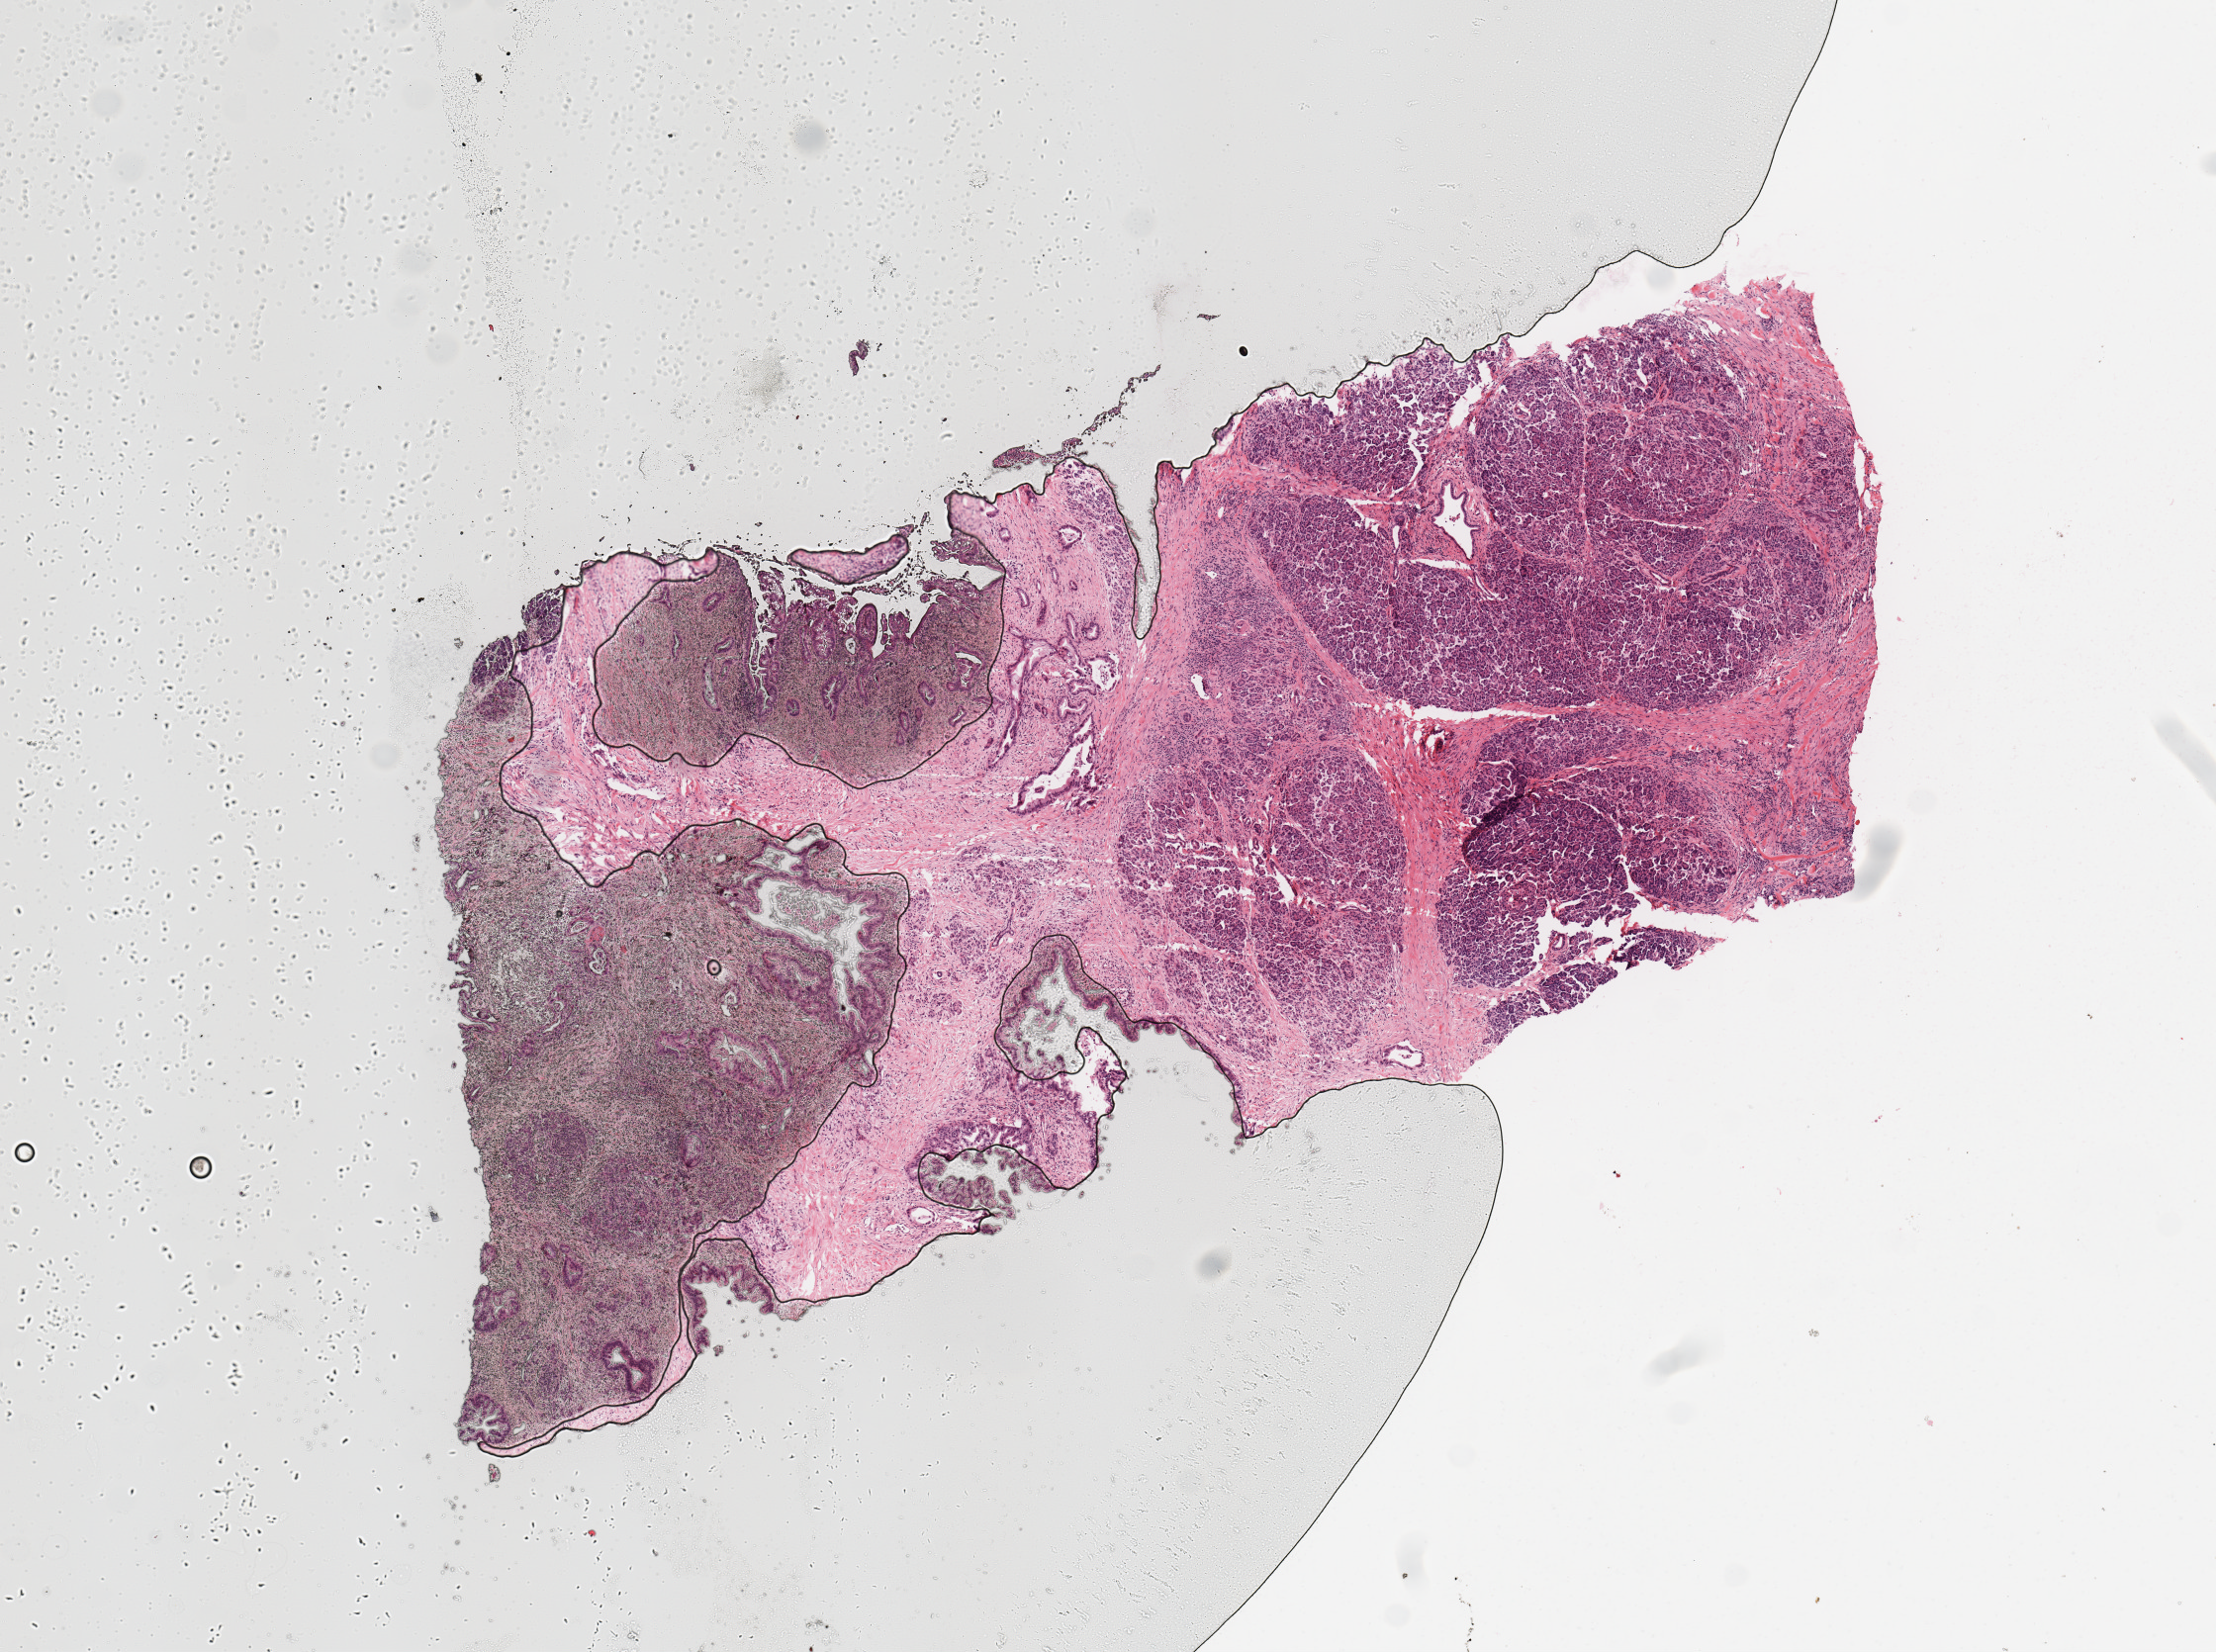
Digitized H&E-stained tissue section (whole slide), shown as a low-resolution overview of the whole scanned area (about 8.9 x 6.6 mm, from a 20x scan). Tumour tissue sample, sampled site: pancreas. 31-year-old male patient. Histologic grade: G1 (well differentiated). Composition of this section per pathologist review: tumour nuclei 20%, necrosis 0%.
• primary tumour site (as recorded): body
• diagnosis: Infiltrating duct carcinoma, NOS
• AJCC pathologic stage: IIB